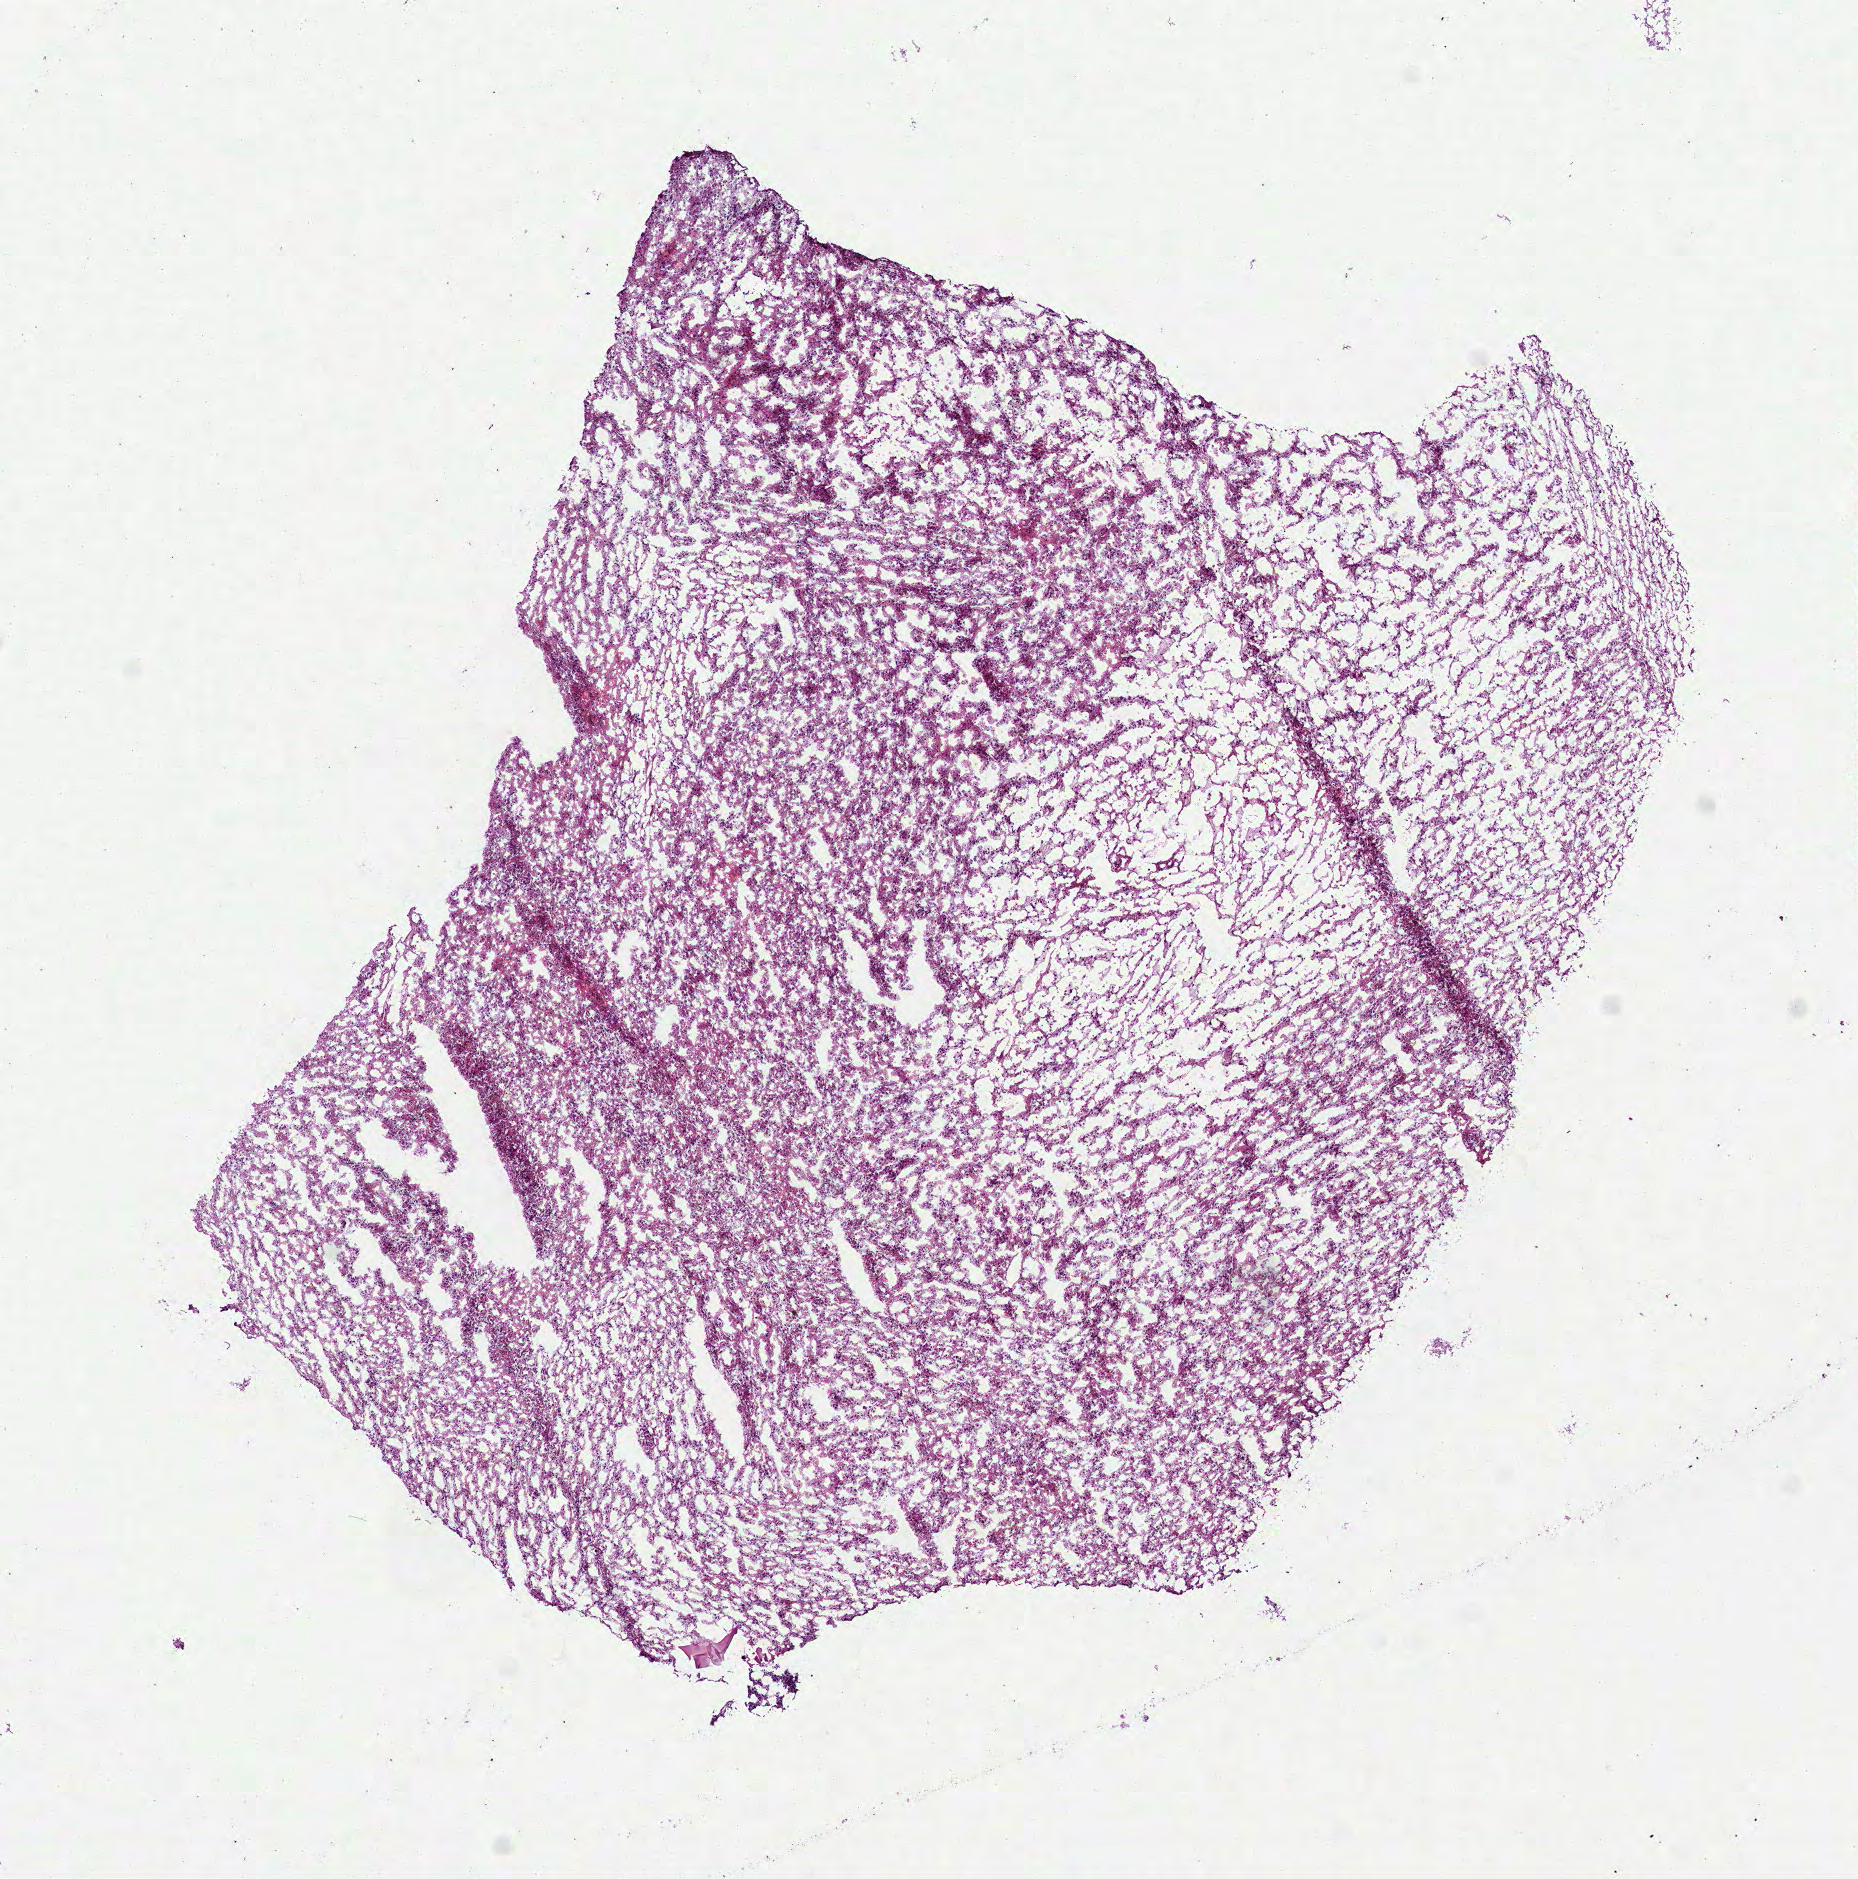
Digitized Hematoxylin and eosin (H&E) stained tissue section (whole slide) — a low-resolution overview of the entire scanned area, about 7.5 x 7.6 mm (acquisition: 40x scan). Frozen section from the bottom of the tissue portion. Primary tumour sample from the brain. Female, age 64 years at initial diagnosis.
Histologic diagnosis: Glioblastoma.